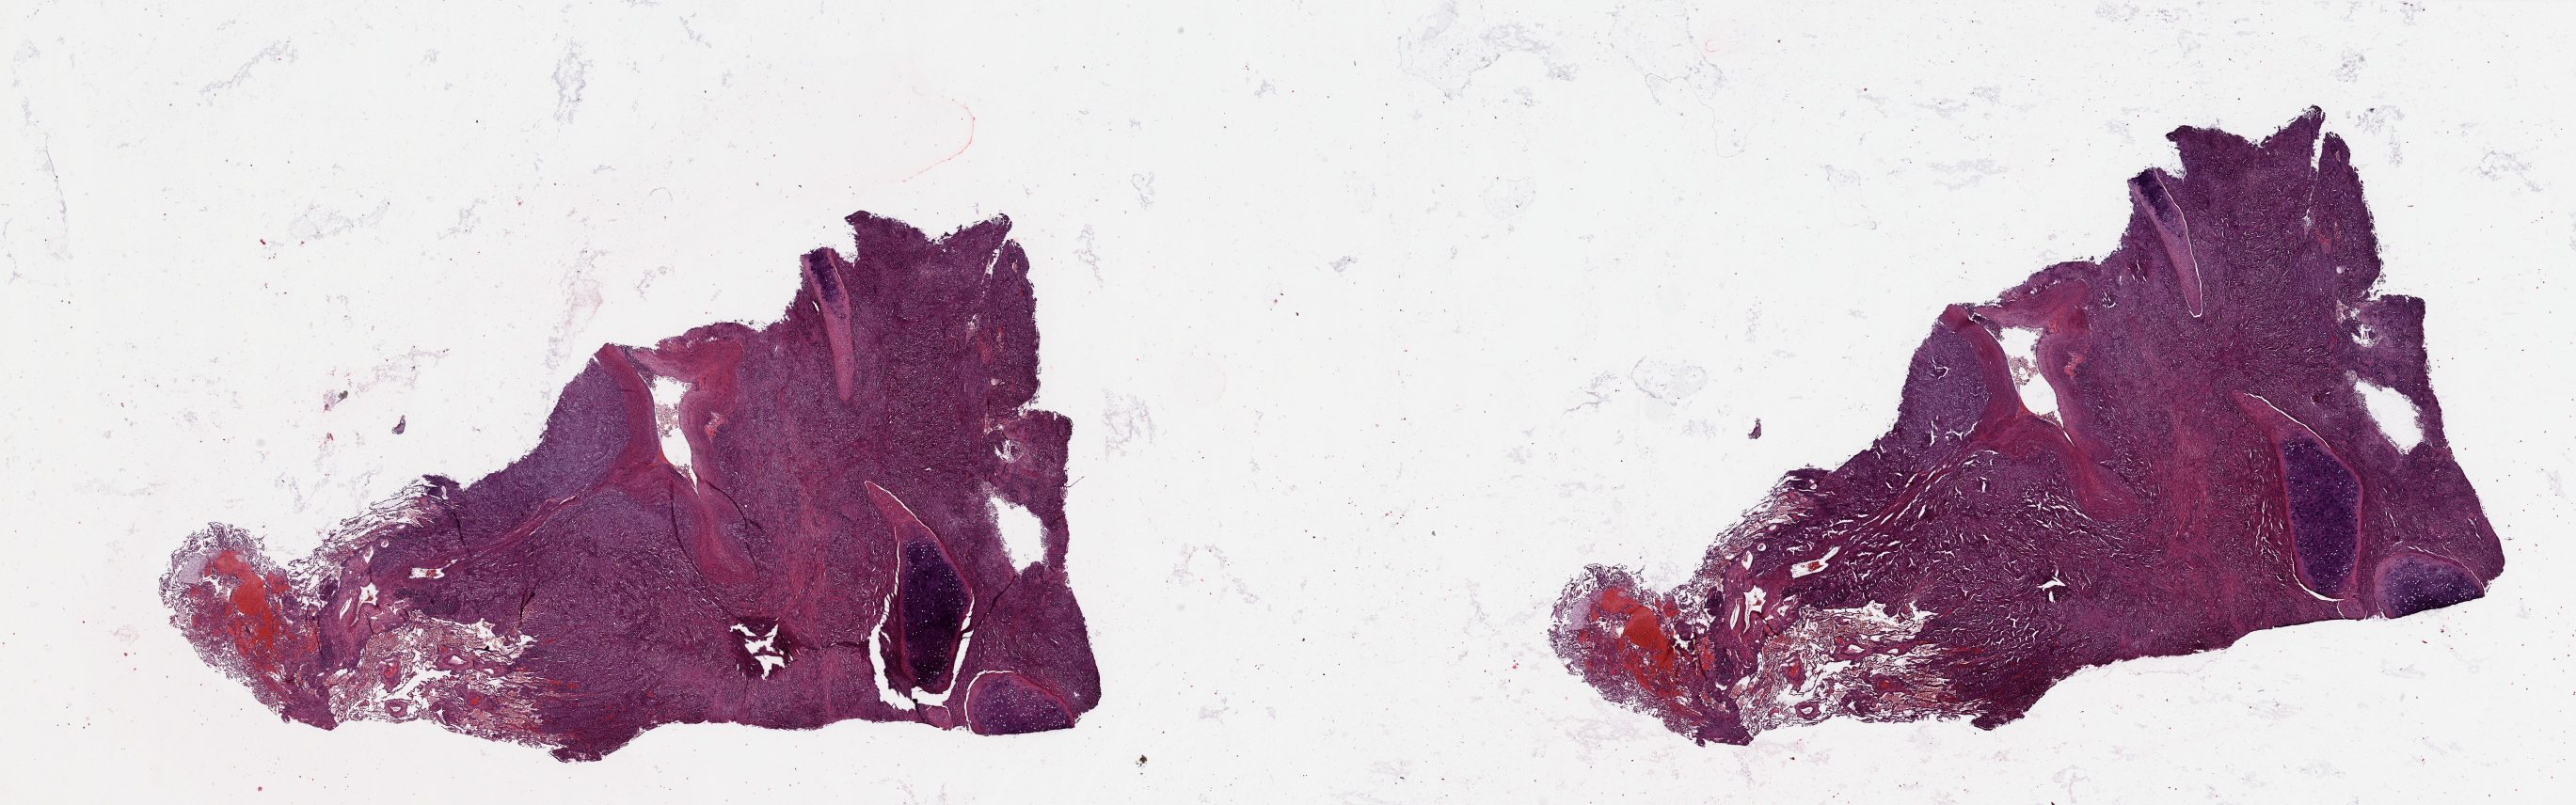
Digitized Hematoxylin and eosin (H&E) stained tissue section (whole slide), whole scanned area (about 43.3 x 13.5 mm) shown as a low-resolution overview, lung, tumour tissue. 72-year-old male patient. Histologic grade: G3 (poorly differentiated).
• AJCC pathologic stage: IB
• diagnosis: Adenocarcinoma, NOS
• primary tumour site (as recorded): left upper lobe